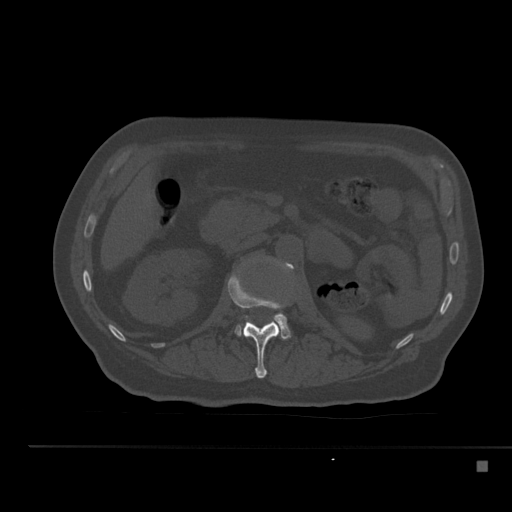
CT including the spine, one axial slice. Position 201 of 517 along the scan axis. 120 kVp. Bone window (W 1800 / L 400 HU). 1.5 mm slice thickness. 512 × 512 image matrix, field of view 408 × 408 mm. Patient: male, 70 years. Case-level facts recorded for this patient, not image findings: primary cancer: renal.
Structures marked on this image (semi-automatically segmented with operator editing):
- L1 vertebra: bounding box (x1, y1, x2, y2) in pixels: (228, 271, 285, 379)
- L2 vertebra: (235, 260, 293, 340)